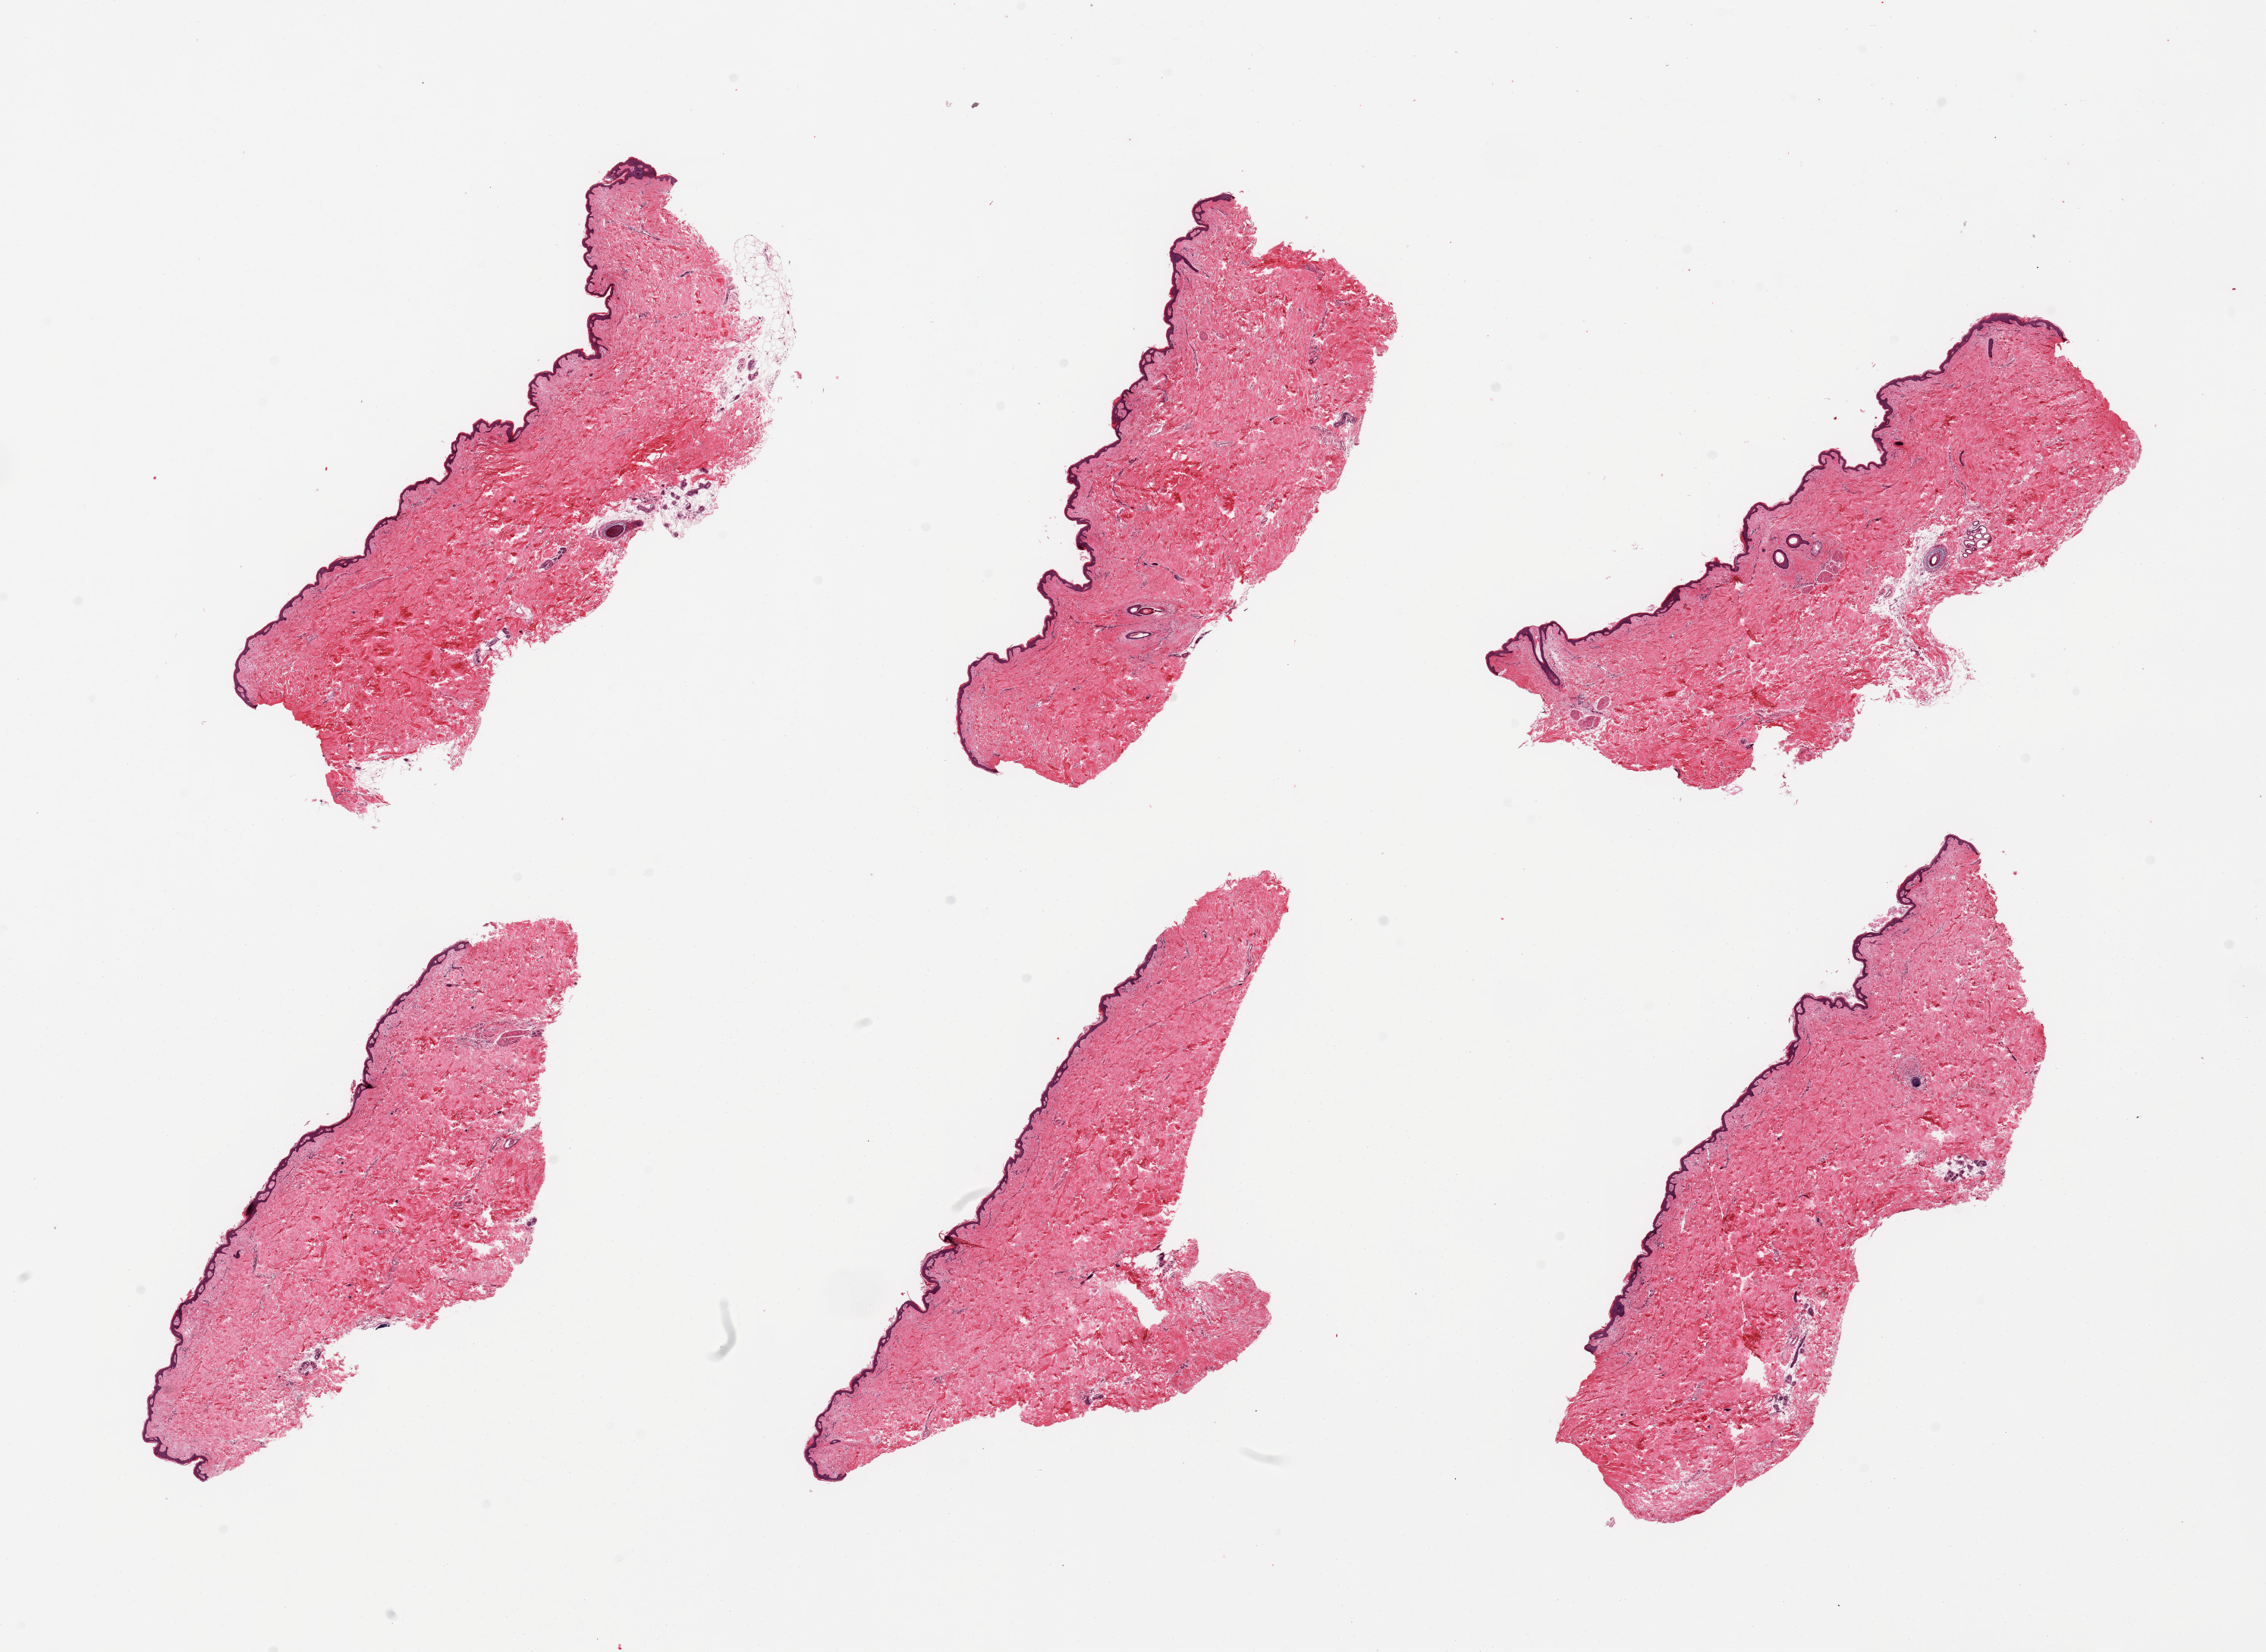
Digitized hematoxylin and eosin (H&E)-stained section, whole scanned area (about 23.6 x 17.2 mm, slide scanned at 20x) shown as a low-resolution overview, PAXgene-fixed paraffin-embedded (PFPE) section, section of skin of suprapubic region (target tissue), donor tissue sample. Donor: female.
• review note (as recorded): 6 pieces; well trimmed; 1% dermal fat